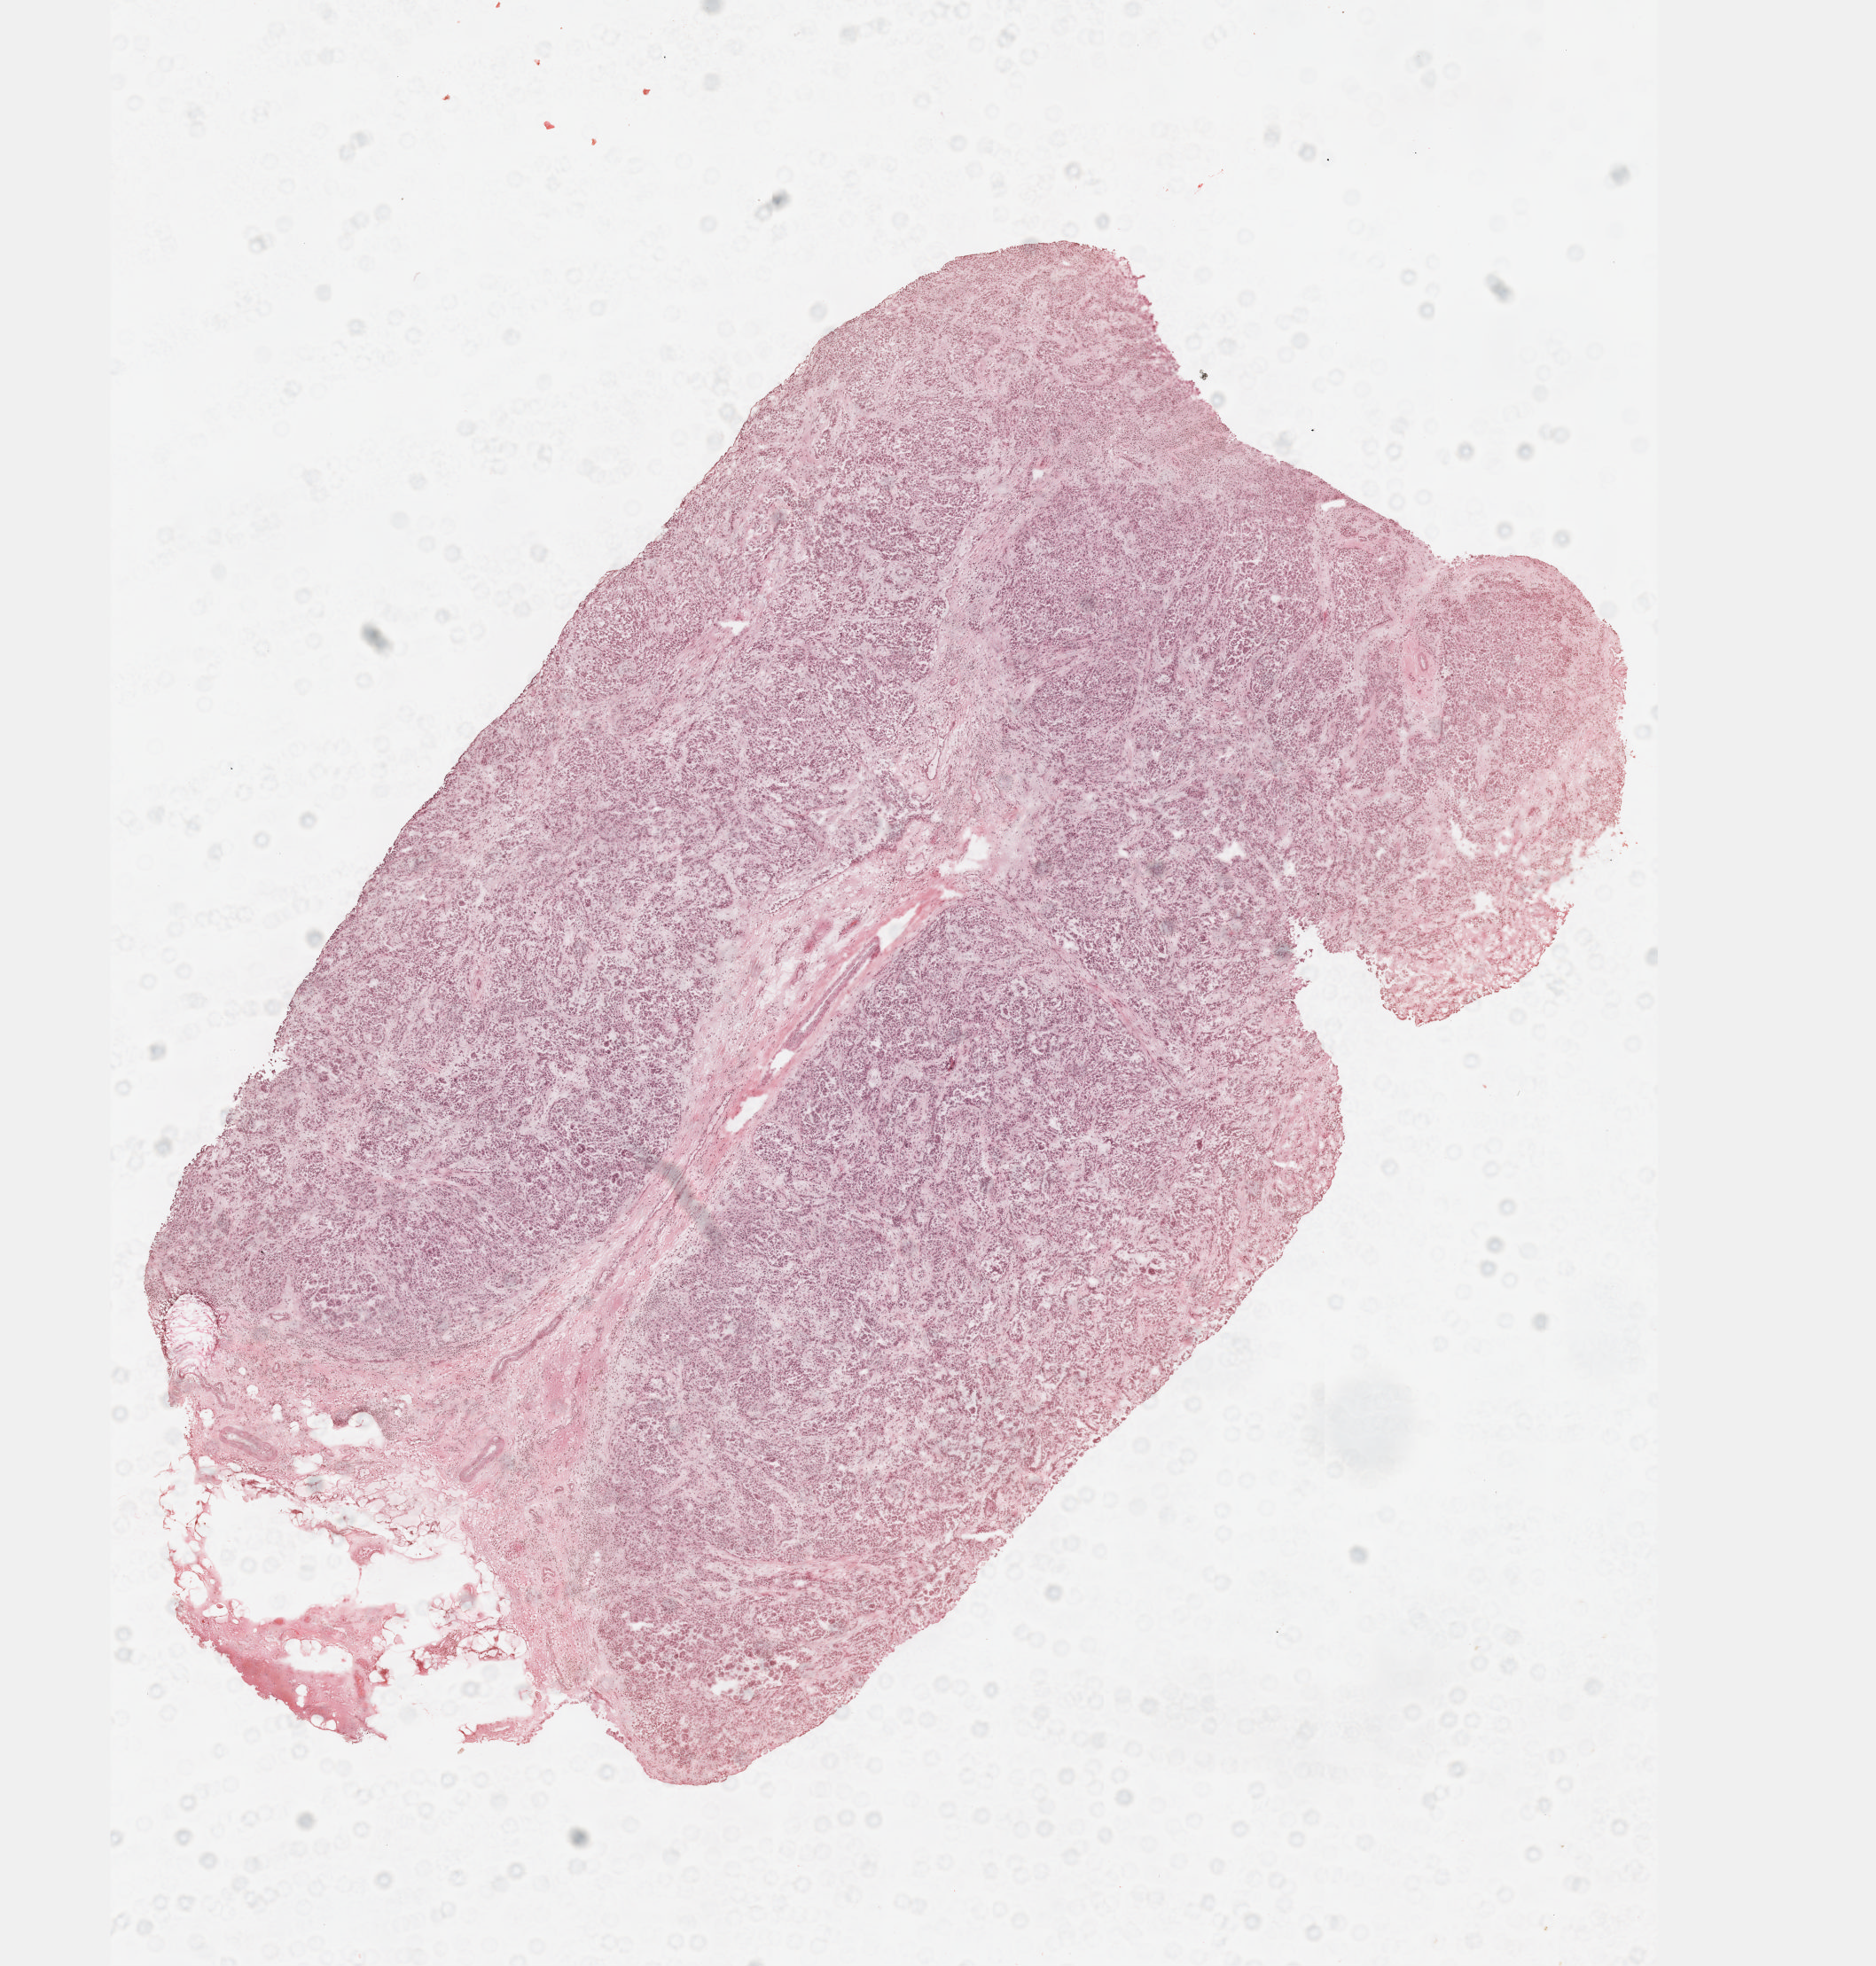
Whole-slide histology image, H&E-stained — shown as a low-resolution overview of the whole scanned area (about 8.6 x 9.0 mm, acquisition: 40x scan). Frozen section from the top of the tissue portion. Sample: primary tumour, mesothelium. Male patient; age at initial diagnosis 51 years. Pathologist review of this section (percent, as recorded): tumour cells 70%, tumour nuclei 70%, normal cells 0%, stromal cells 30%, necrosis 0%. Inflammatory infiltration, as recorded: lymphocyte infiltration 40%, monocyte infiltration 20%, neutrophil infiltration 20%.
• laterality: right
• TNM: T3 N2 MX
• AJCC pathologic stage: III (7th edition)
• diagnosis: Epithelioid mesothelioma, malignant (pleura, NOS)